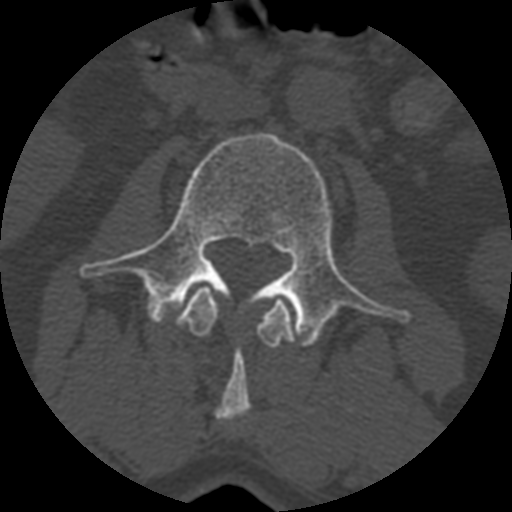
CT including the spine, one axial slice; position 313 of 399 along the scan axis; reconstruction kernel STANDARD; 120 kVp; bone window (W 1800 / L 400 HU); 1.25 mm slice thickness; 512 × 512 image matrix, field of view 160 × 160 mm. Patient age 71 years. Case-level facts recorded for this patient, not image findings: primary cancer: prostate.
Structures marked on this image (semi-automatic segmentation, software-assisted and operator-edited):
- L2 vertebra: box from (x=176, y=286) to (x=293, y=426) px
- L3 vertebra: (x=79, y=132)–(x=406, y=346)